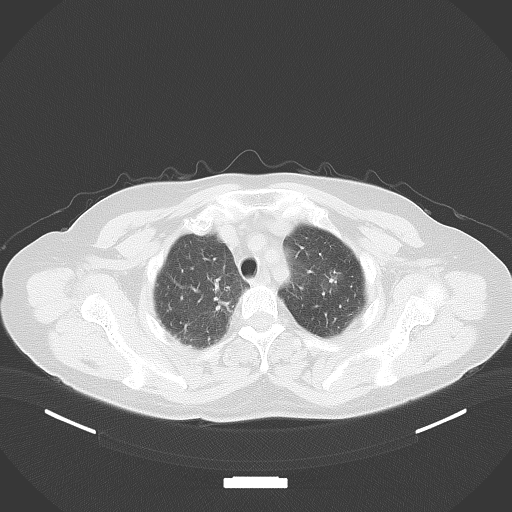
Chest CT, one axial slice; position 71 of 116 along the scan axis; 120 kVp; lung window (W 1500 / L -600 HU); 512 × 512 image matrix, field of view 400 × 400 mm. Female patient, age 64 years. Case-level facts recorded for this patient, not image findings: clinical TNM (as recorded): T1c N0 M0.
Outlined on this slice (rectangle marked by the reading radiologist):
- lung tumour (recorded histology: adenocarcinoma): bounding box <326,270,342,288> (left, top, right, bottom; pixels)